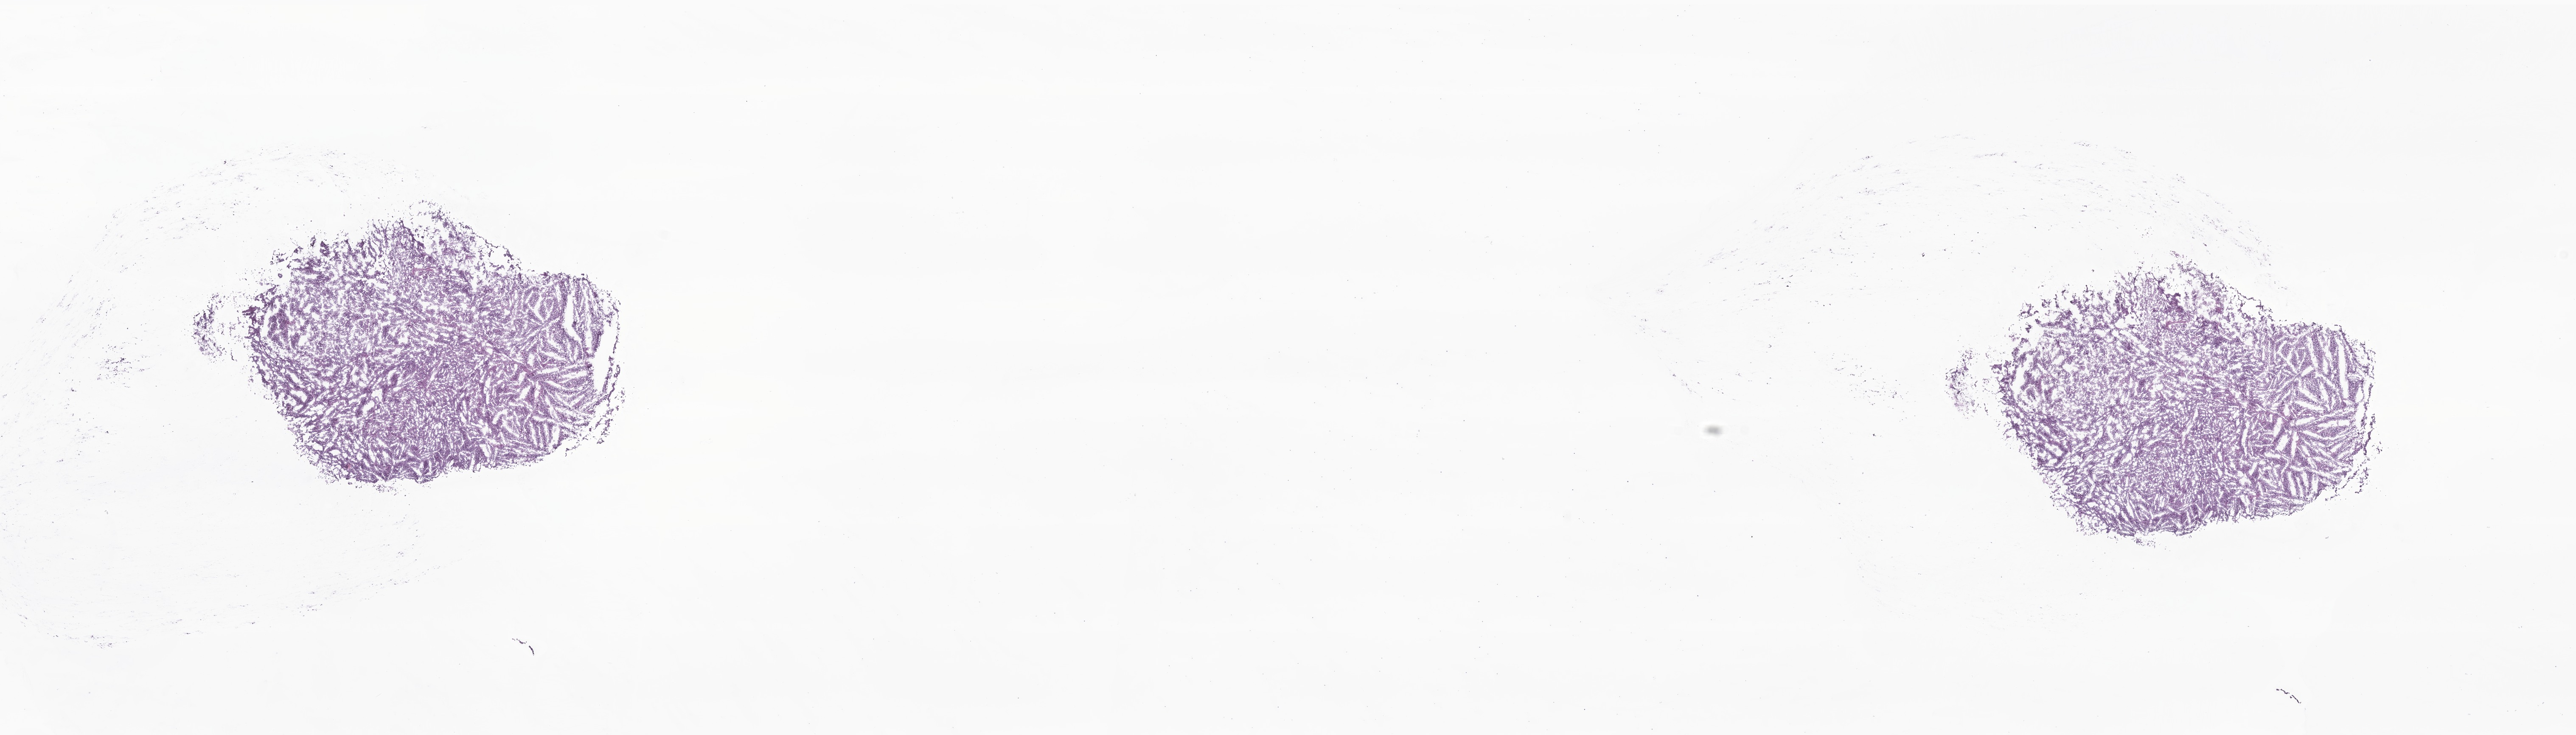
Whole-slide image, haematoxylin and eosin stain of tumor tissue from the brain, a low-resolution overview of the entire scanned area, about 25.6 x 7.3 mm, frozen section (OCT-embedded). Female patient, age 241 days.
Diagnosis: Medulloblastoma, NOS.